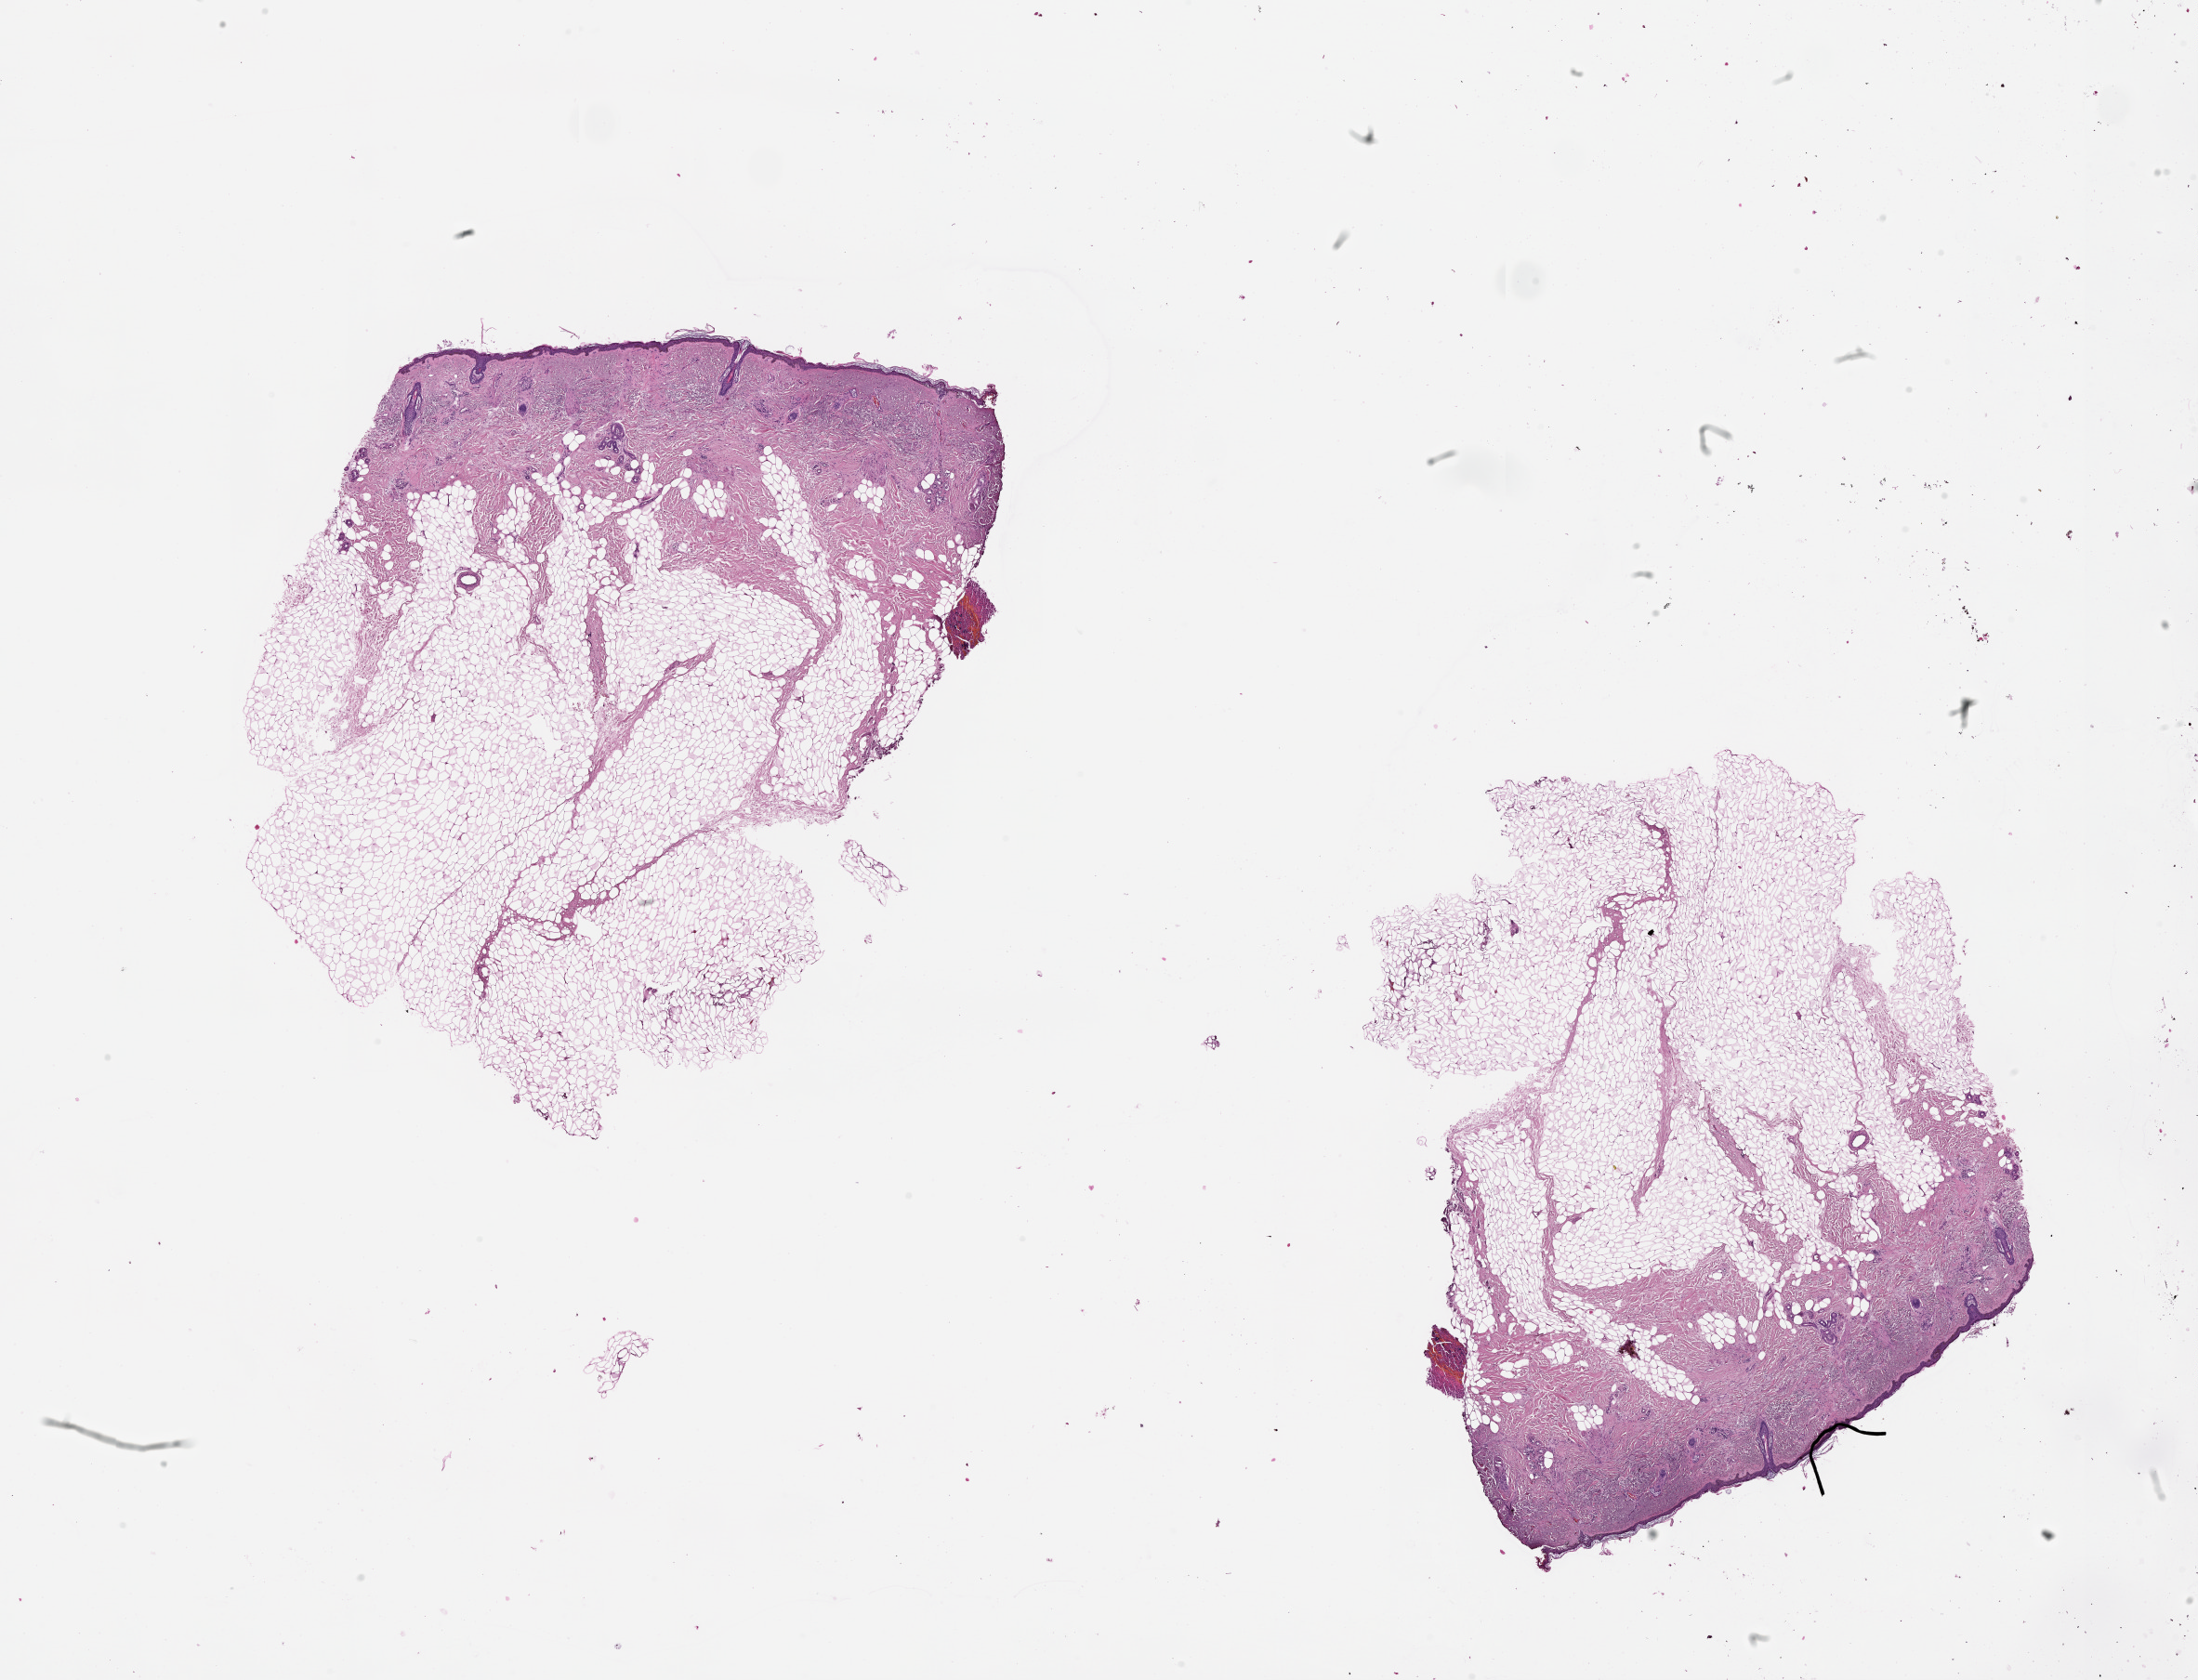
Digitized H&E tissue section (whole slide) — whole scanned area (about 19.0 x 14.6 mm) shown as a low-resolution overview, normal (non-tumour) tissue sample, sampled site: head & neck. Female, 75 y/o.
• this section: normal (non-tumour) tissue from the same patient
• patient diagnosis: Malignant melanoma, NOS